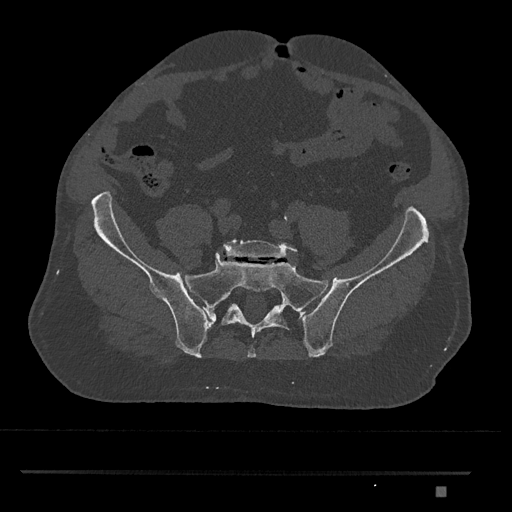
CT including the spine, one axial slice. Slice 505 of 1134 in the series (ordered by position). Bone window (W 1800 / L 400 HU). 0.5 mm slice thickness. 512 × 512 image matrix, field of view 429 × 429 mm. Male patient, age 65 years. From the clinical record (not read from this slice): primary cancer: prostate.
Annotated regions visible in this slice (semi-automatically segmented with operator editing):
- L5 vertebra: bounding box (x1, y1, x2, y2) in pixels: (222, 239, 298, 259)